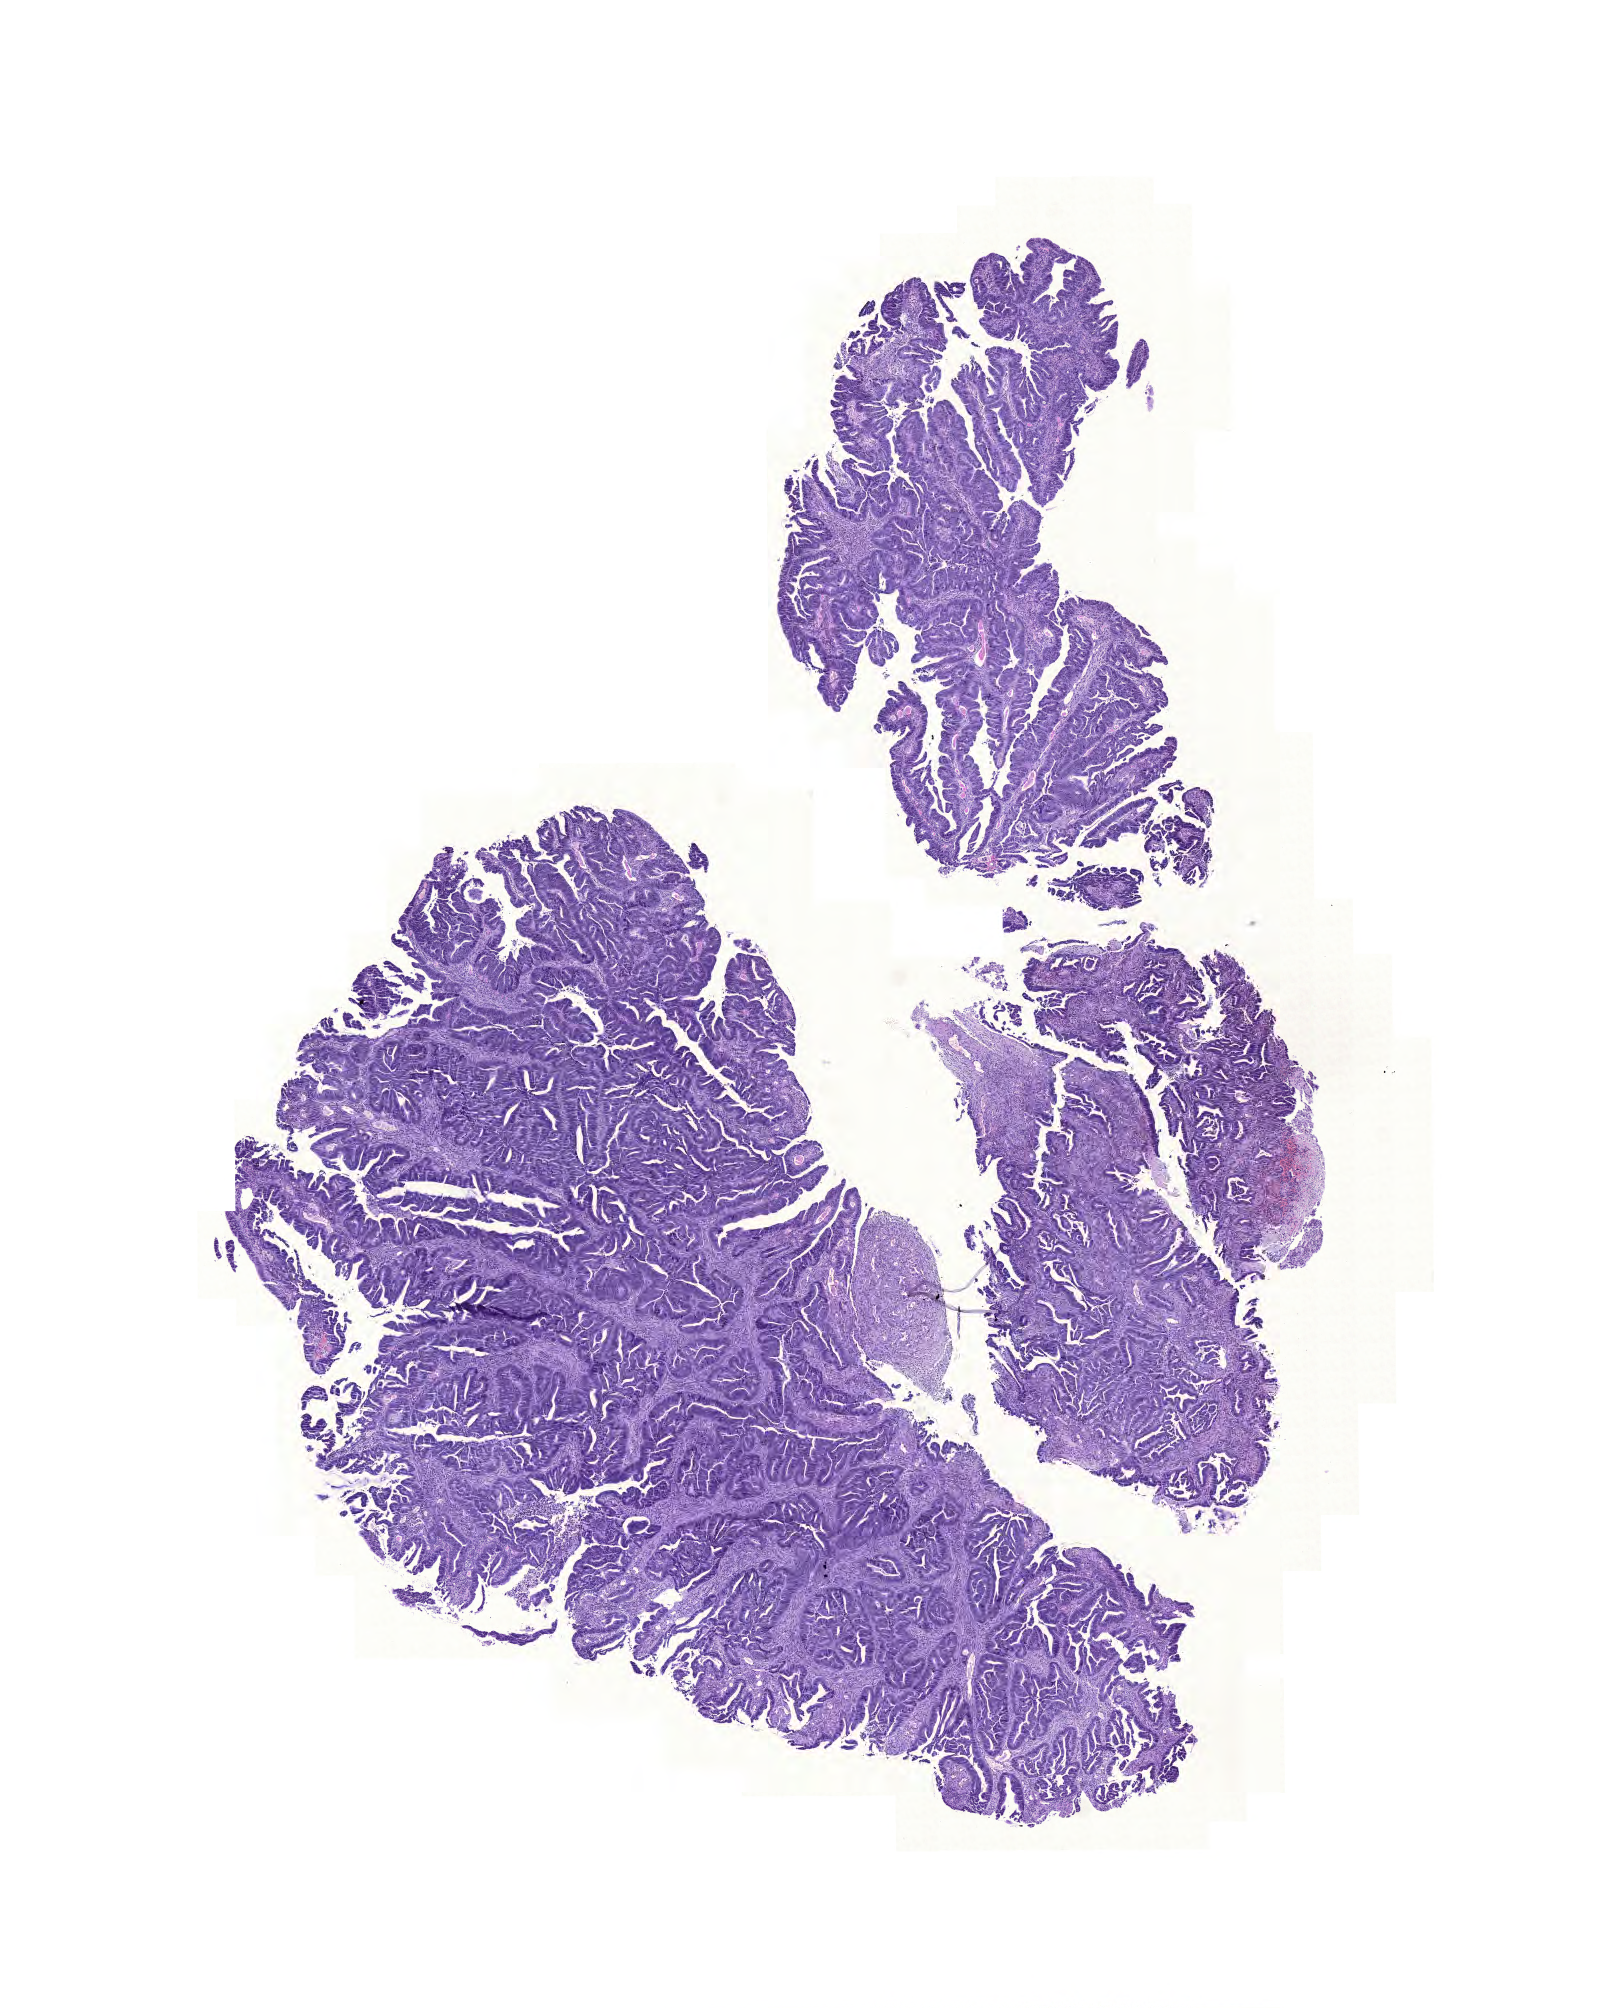
Digitized Hematoxylin and eosin (H&E) stained tissue section (whole slide) — a low-resolution overview of the entire scanned area, about 12.0 x 14.9 mm (slide scanned at 20x). FFPE section. Rectum, primary tumour sample. Male patient; age at initial diagnosis 65 years.
Diagnosis: Adenocarcinoma, NOS.